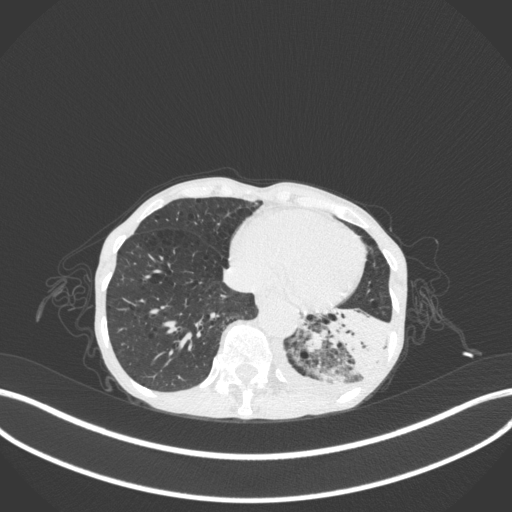
Chest CT, one axial slice. Slice 54 of 347 in the series (ordered by position). Lung window (W 1500 / L -600 HU). 512 × 512 image matrix, field of view 400 × 400 mm. Female patient, age 70 years. From the clinical record (not read from this slice): clinical TNM (as recorded): T3 N0 M0.
Annotated regions visible in this slice (bounding box drawn by a radiologist):
- lung tumour (recorded histology: small cell carcinoma): bounding box [x1, y1, x2, y2] px = [300, 295, 394, 393]